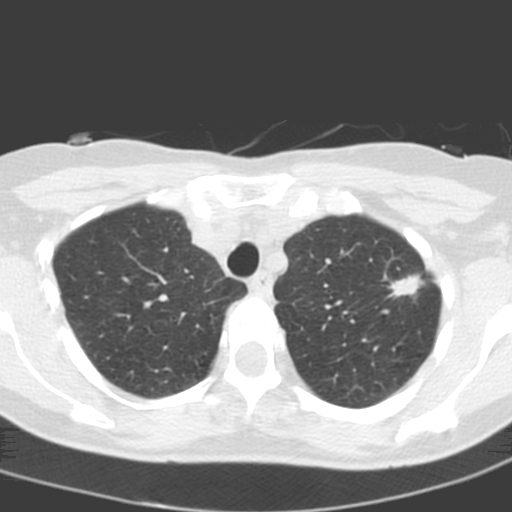
Low-dose screening chest CT, one axial slice. Position 156 of 193 along the scan axis. 120 kVp. Lung window (W 1500 / L -600 HU). 3.2 mm slice thickness. 512 × 512 image matrix, field of view 272 × 272 mm.
Structures marked on this image (manually delineated by an expert):
- lesion 1 (tumor, upper lobe of left lung): bounding box (x1, y1, x2, y2) in pixels: (389, 274, 424, 298)